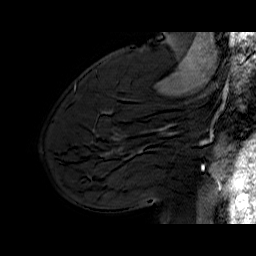
Breast MRI (dynamic contrast-enhanced), one sagittal slice. Slice 44 of 70 in the series (ordered by position). Dynamic contrast-enhanced series, time point 2 of 6 at this slice position (early post-contrast). 1.5 T. TE 6.5 ms, TR 33 ms. 4 mm slice thickness. 256 × 256 image matrix, field of view 200 × 200 mm. Female patient. Case-level facts recorded for this patient, not image findings: setting: breast cancer imaged before/during neoadjuvant chemotherapy; receptor status: HER2-positive.
Outlined on this slice (semi-automatically segmented with operator editing):
- analysis volume of interest (the breast-tissue region the enhancement analysis was run in; not a lesion): bounding box <113,112,174,170> (left, top, right, bottom; pixels)
- tumour enhancement mask (voxels above the 100 % enhancement threshold inside the analysis volume of interest): <163,124,174,134>